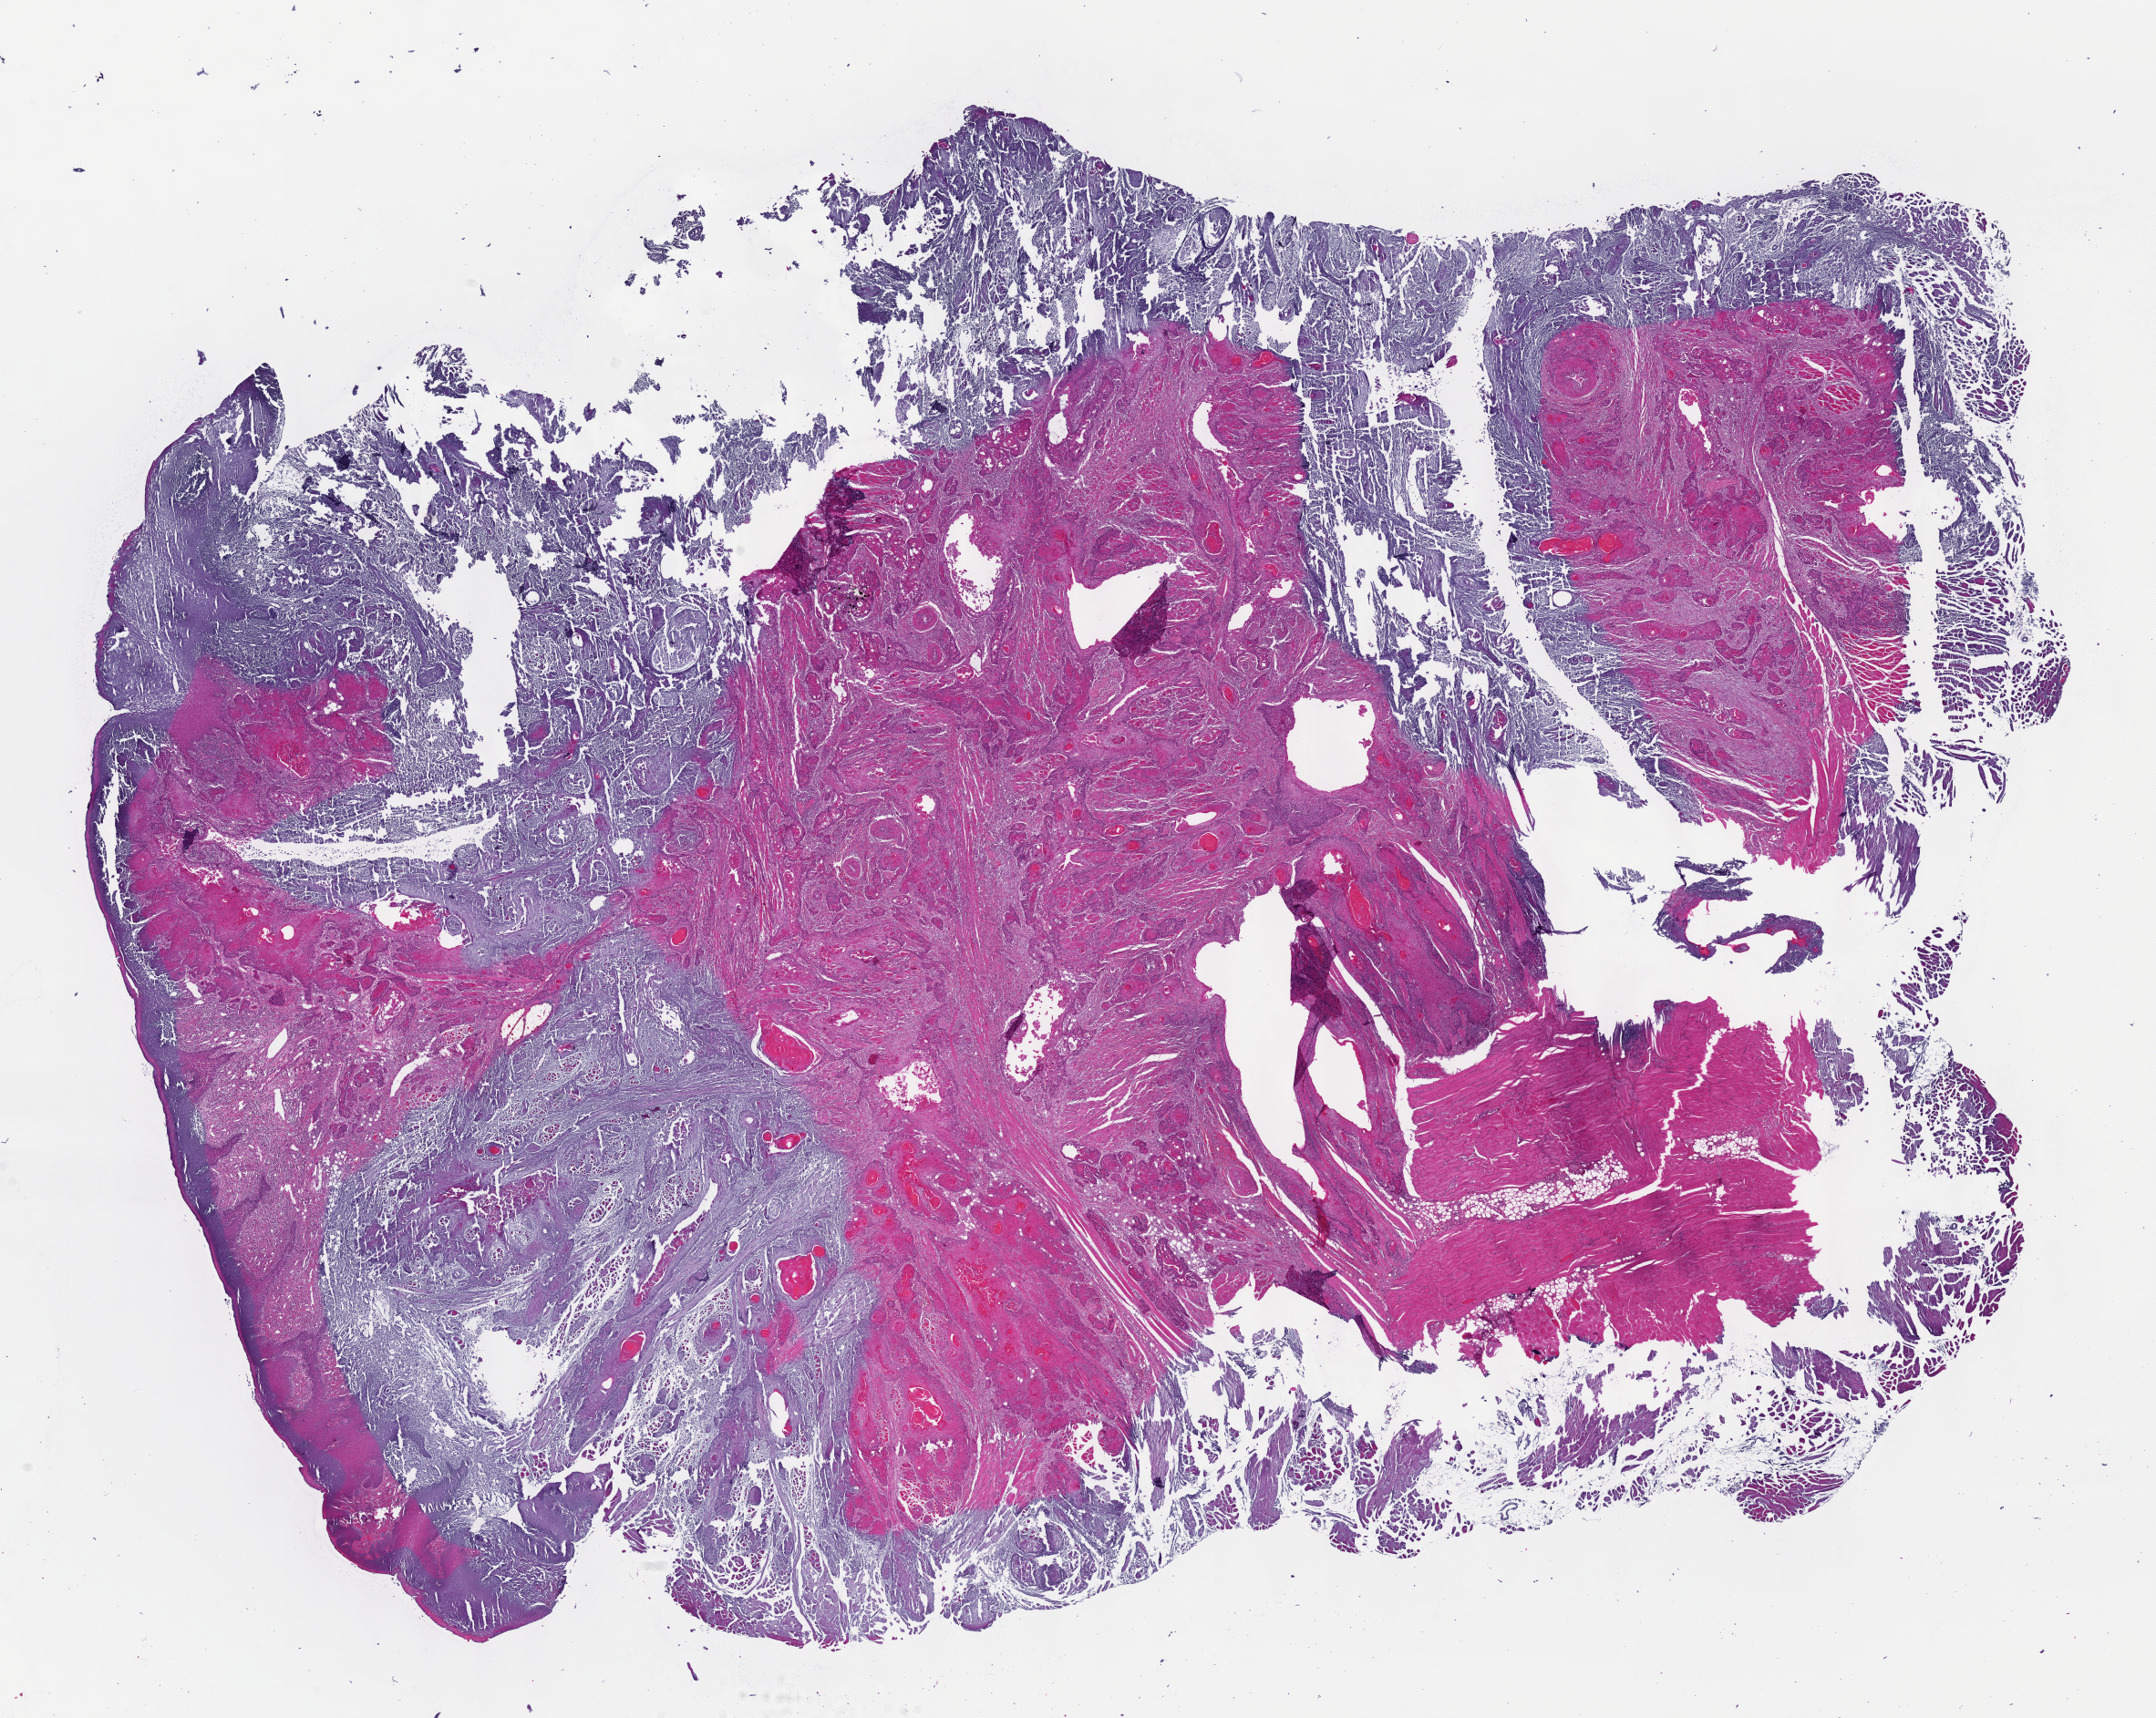
Digitized H&E-stained tissue section (whole slide) — low-resolution overview of the scanned area, about 19.1 x 15.2 mm (slide scanned at 40x), formalin-fixed paraffin-embedded (FFPE) diagnostic section, head and neck, primary tumour sample. Patient: male, age at initial diagnosis 74 years.
Diagnosis: Squamous cell carcinoma, NOS (base of tongue, NOS).